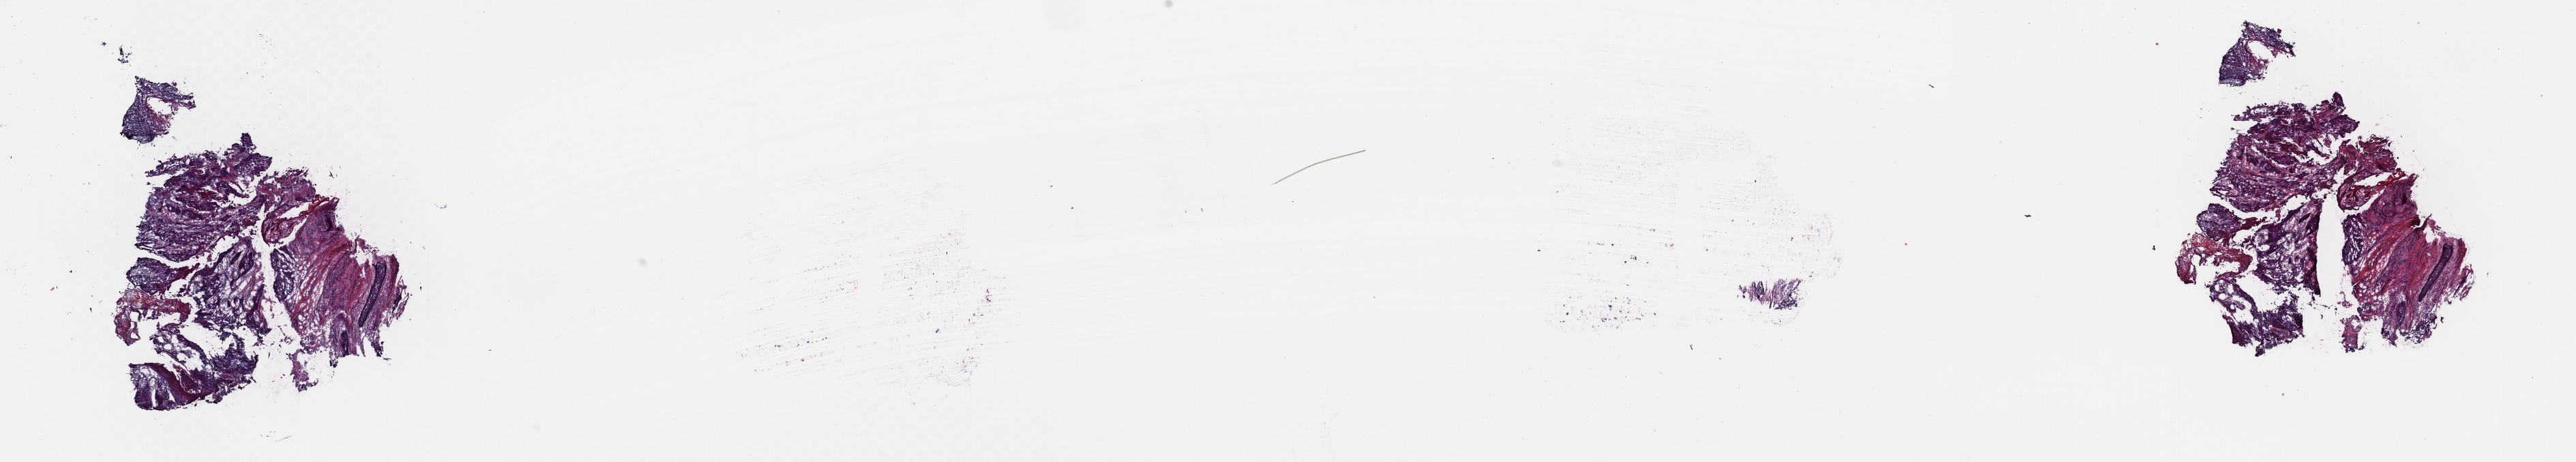
Digitized Hematoxylin and eosin (H&E) stained tissue section (whole slide) — low-resolution overview of the scanned area, about 29.8 x 5.3 mm (slide scanned at 40x). Frozen section. Primary tumour sample from the head and neck. Male patient; age at initial diagnosis 59 years. Histologic grade: G1 (well differentiated). Slide review estimates, as recorded: tumour cells 80%, tumour nuclei 75%, normal cells 20%, stromal cells 0%, necrosis 0%. Infiltration values recorded for this section: lymphocyte infiltration 4%, monocyte infiltration 0%, neutrophil infiltration 0%.
Laterality: left. Histologic diagnosis: Squamous cell carcinoma, NOS (mouth, NOS). AJCC pathologic stage: IVA. TNM: T4 N2b M0.